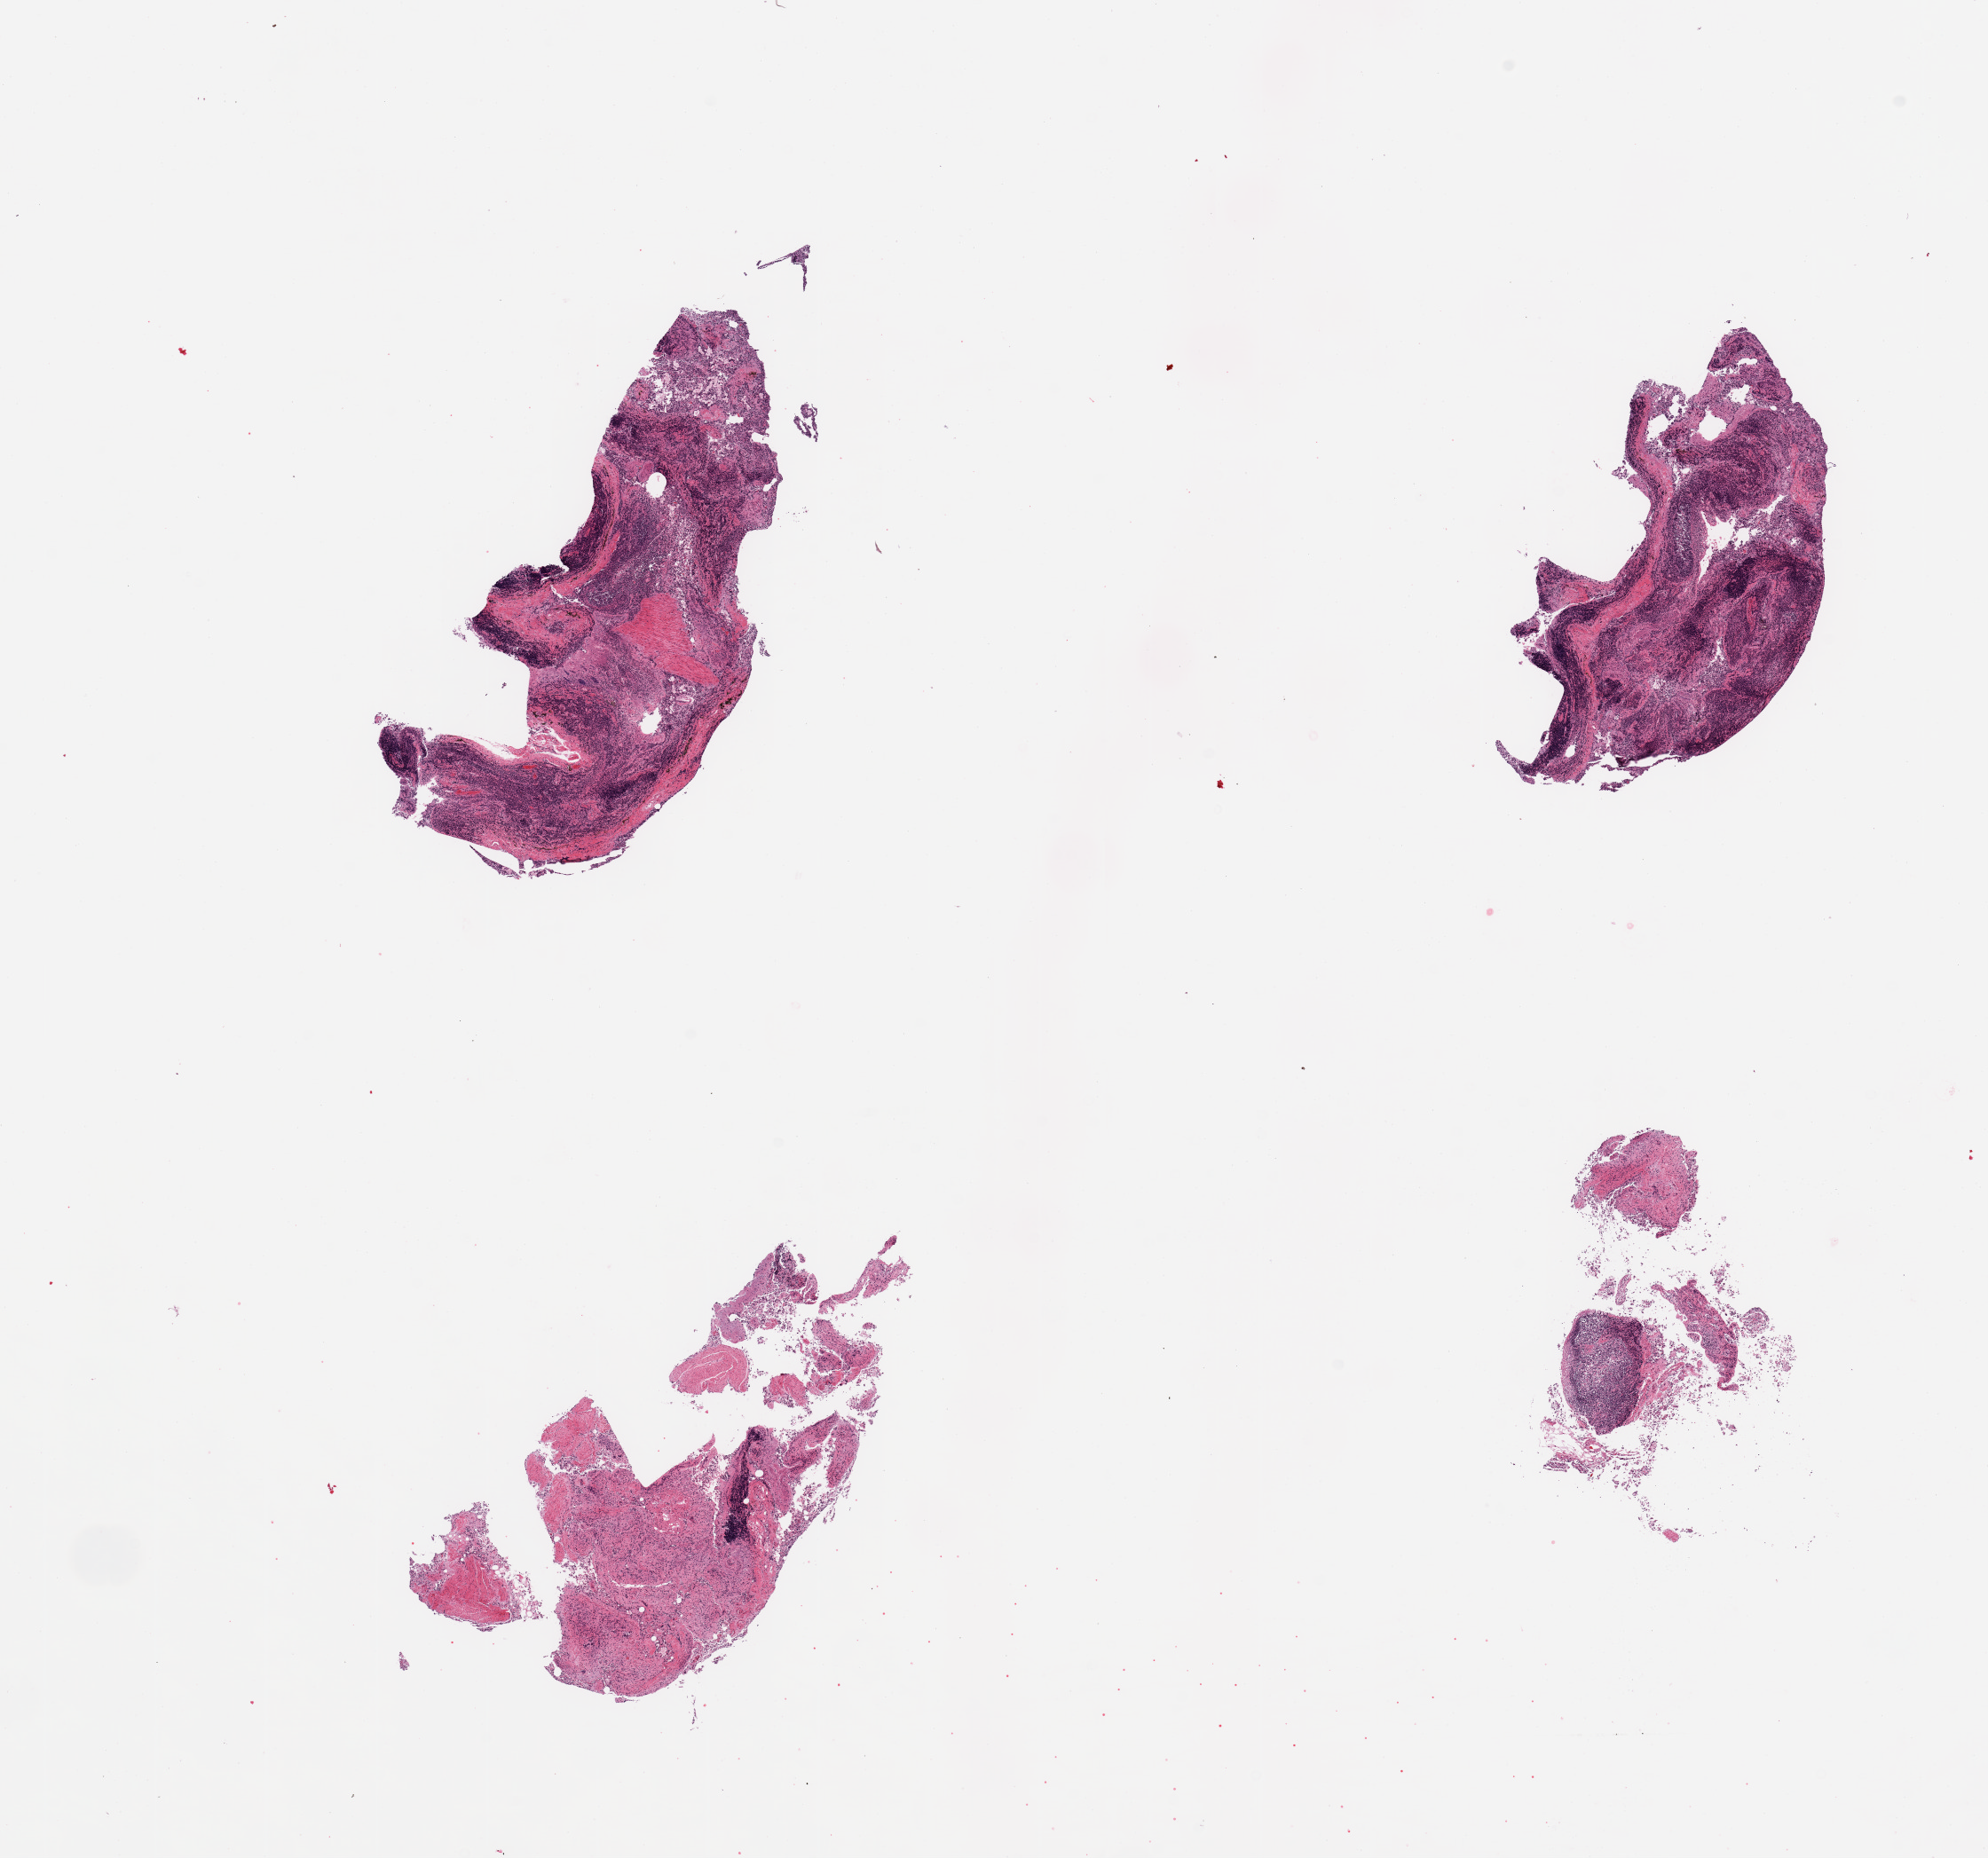
H&E whole-slide image, whole scanned area (about 17.7 x 16.6 mm) shown as a low-resolution overview. PAXgene-fixed, paraffin-embedded tissue. Sampled site (target tissue): ileum. Donor tissue sample. Donor sex: male.
Review note (as recorded): 4 pieces; lymphoid tissue intact, remaining tissue autolyzed; 1 piece has very little lymphoid component.